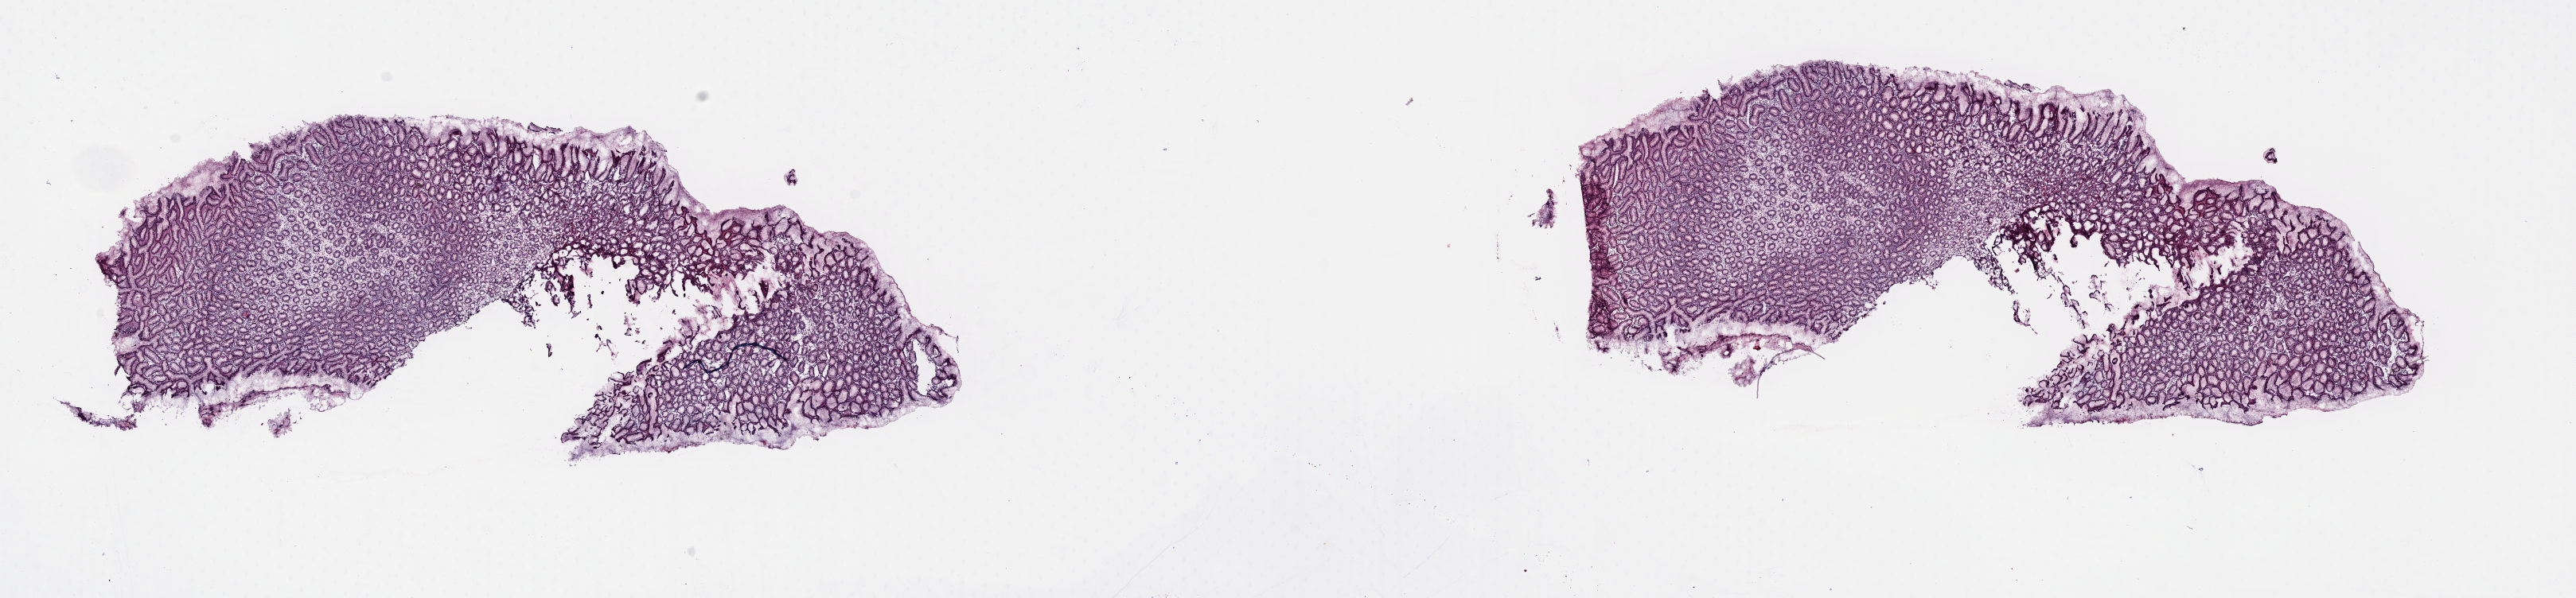
H&E whole-slide image — whole scanned area (about 25.6 x 5.9 mm) shown as a low-resolution overview. Frozen section from the top of the tissue portion. Stomach, solid tissue normal (non-tumour tissue) sample. Patient: female, age at initial diagnosis 53 years. Pathologist review of this section (percent, as recorded): tumour cells 0%, tumour nuclei 0%.
This section: solid tissue normal (non-tumour) sample from the same patient. Patient diagnosis: Tubular adenocarcinoma (gastric antrum).